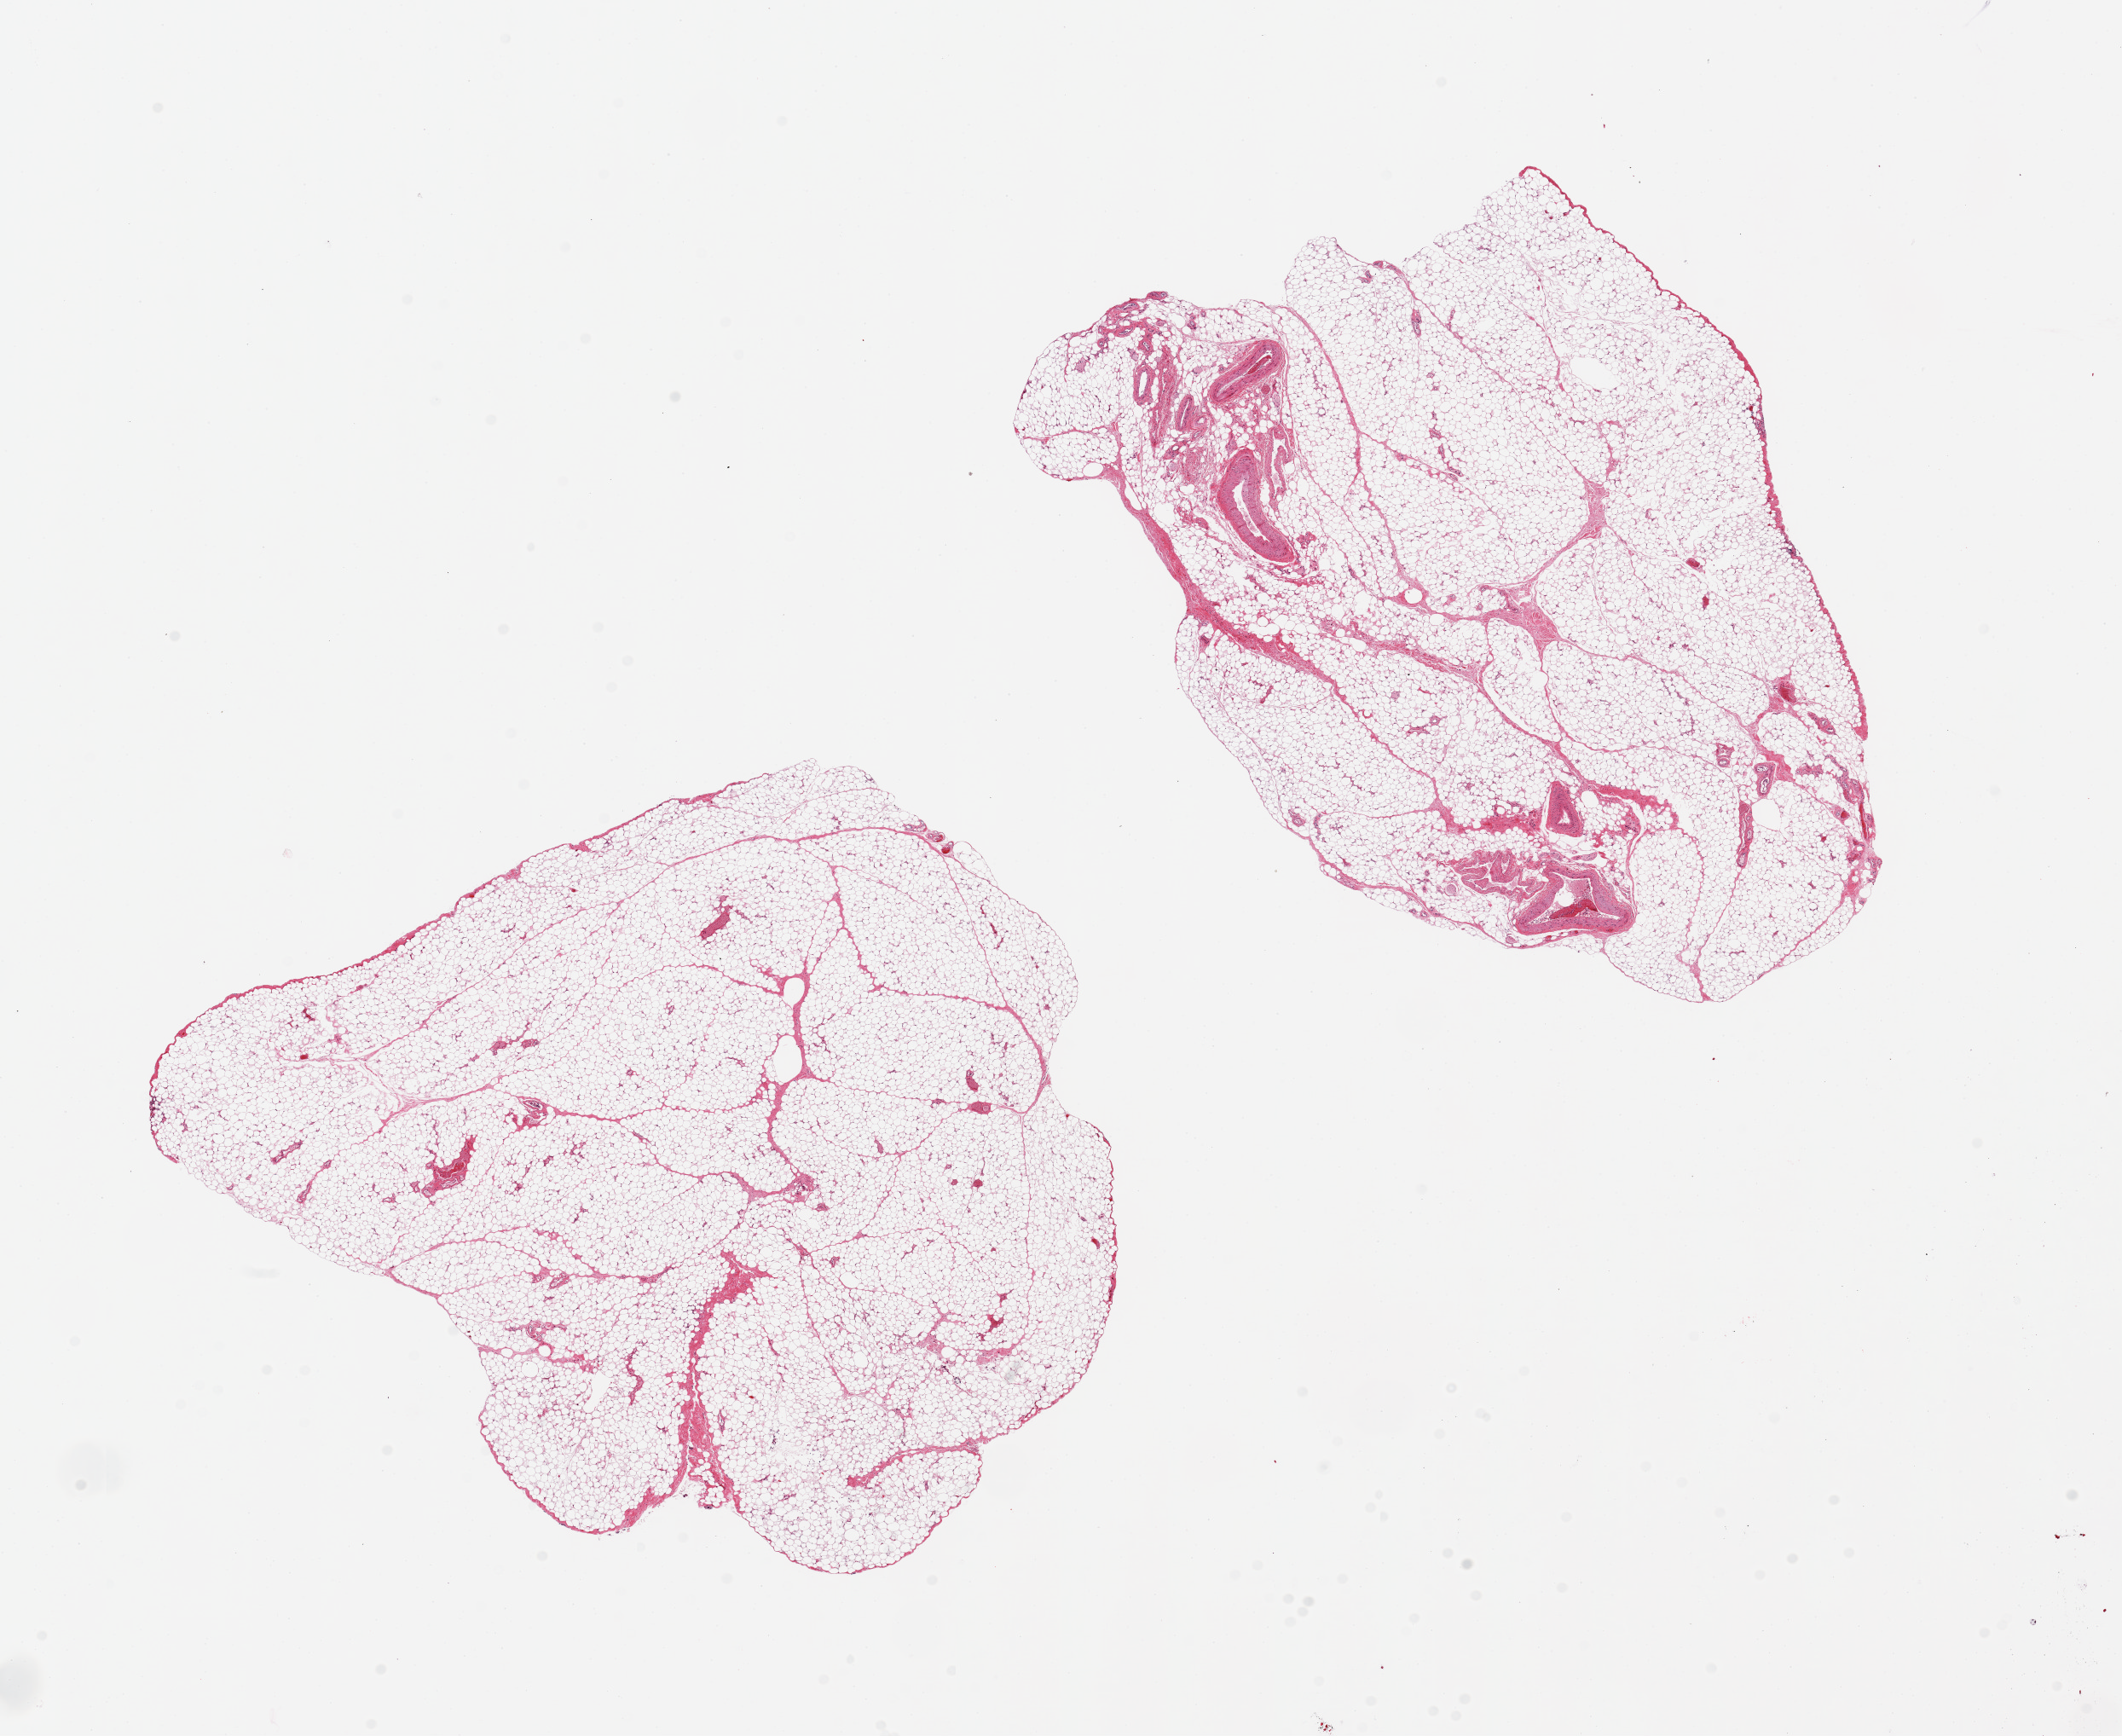
Digitized H&E-stained section, brightfield — shown as a low-resolution overview of the whole scanned area (about 19.7 x 16.1 mm, from a 20x scan). PAXgene-fixed, paraffin-embedded tissue. Section of omentum (target tissue). Donor tissue sample. Donor: male.
Review note (as recorded): 2 pieces, 8x7 & 9x6mm; No artifacts.